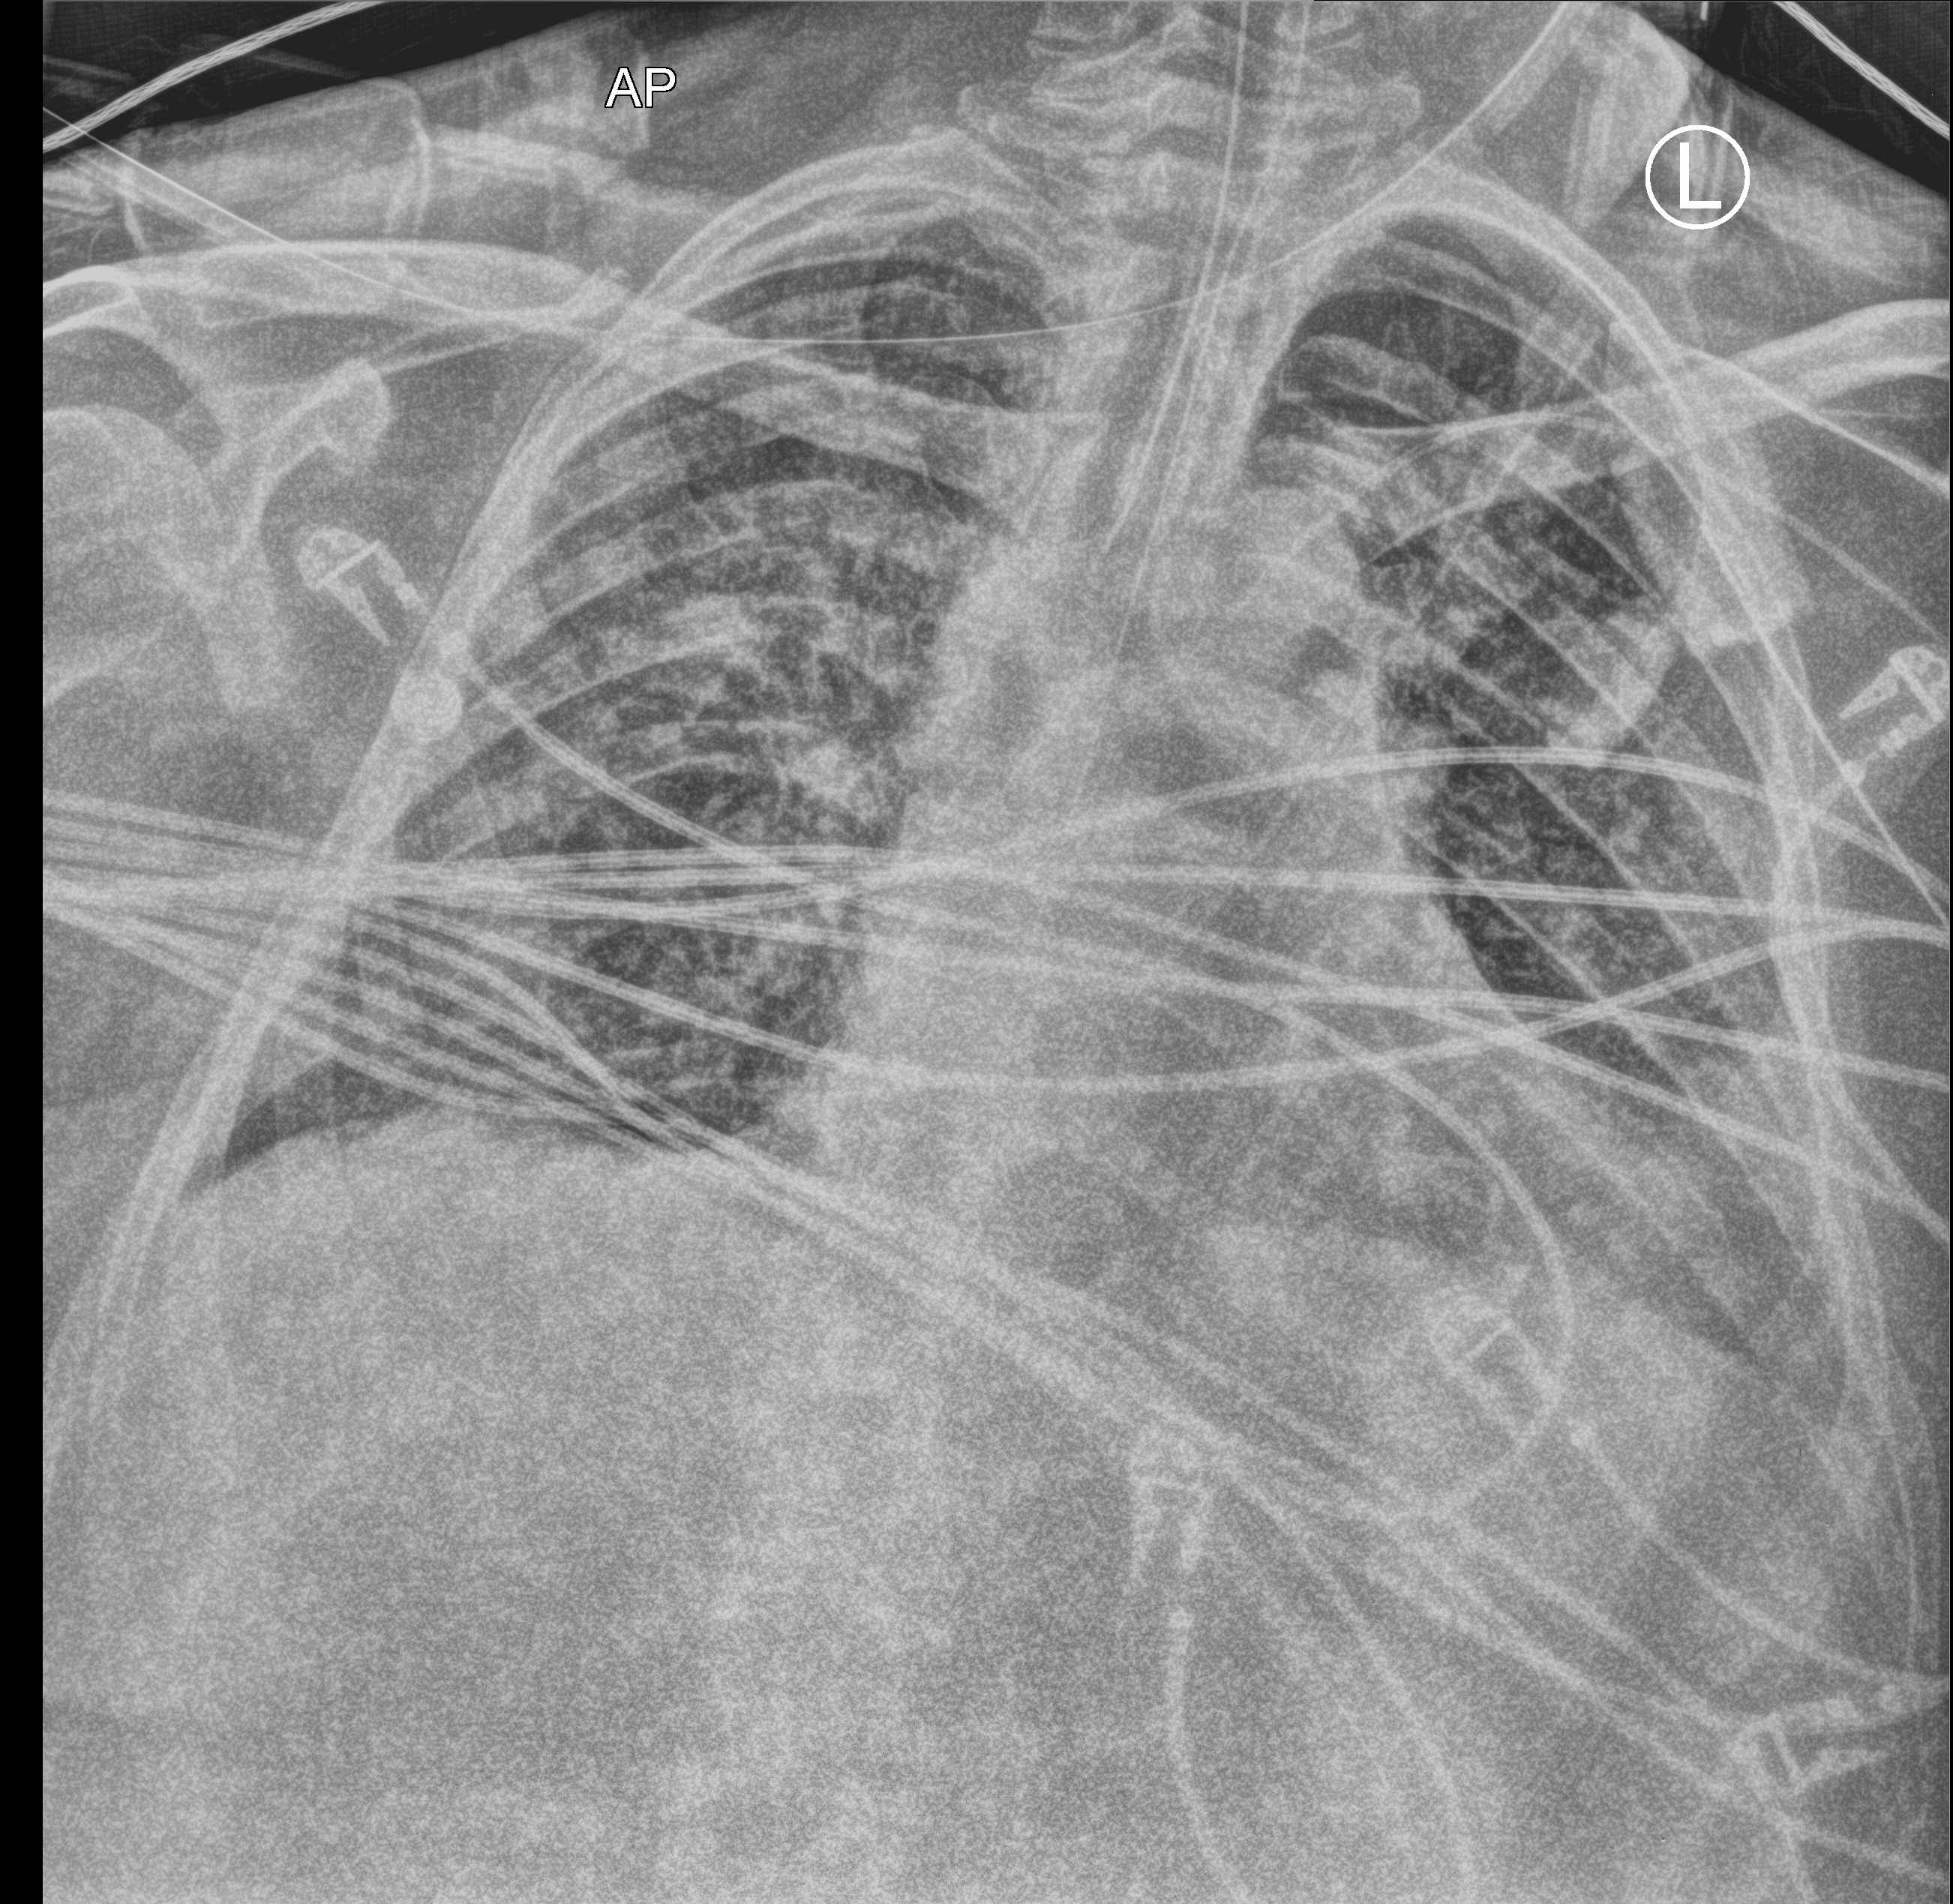
Chest X-ray (portable). Male patient hospitalised with COVID-19, age 18–59 years.
Admission-level facts for this patient (not findings on this image; timing relative to this image not recorded): other chronic lung disease (admission record): no; chronic kidney disease (admission record): no.